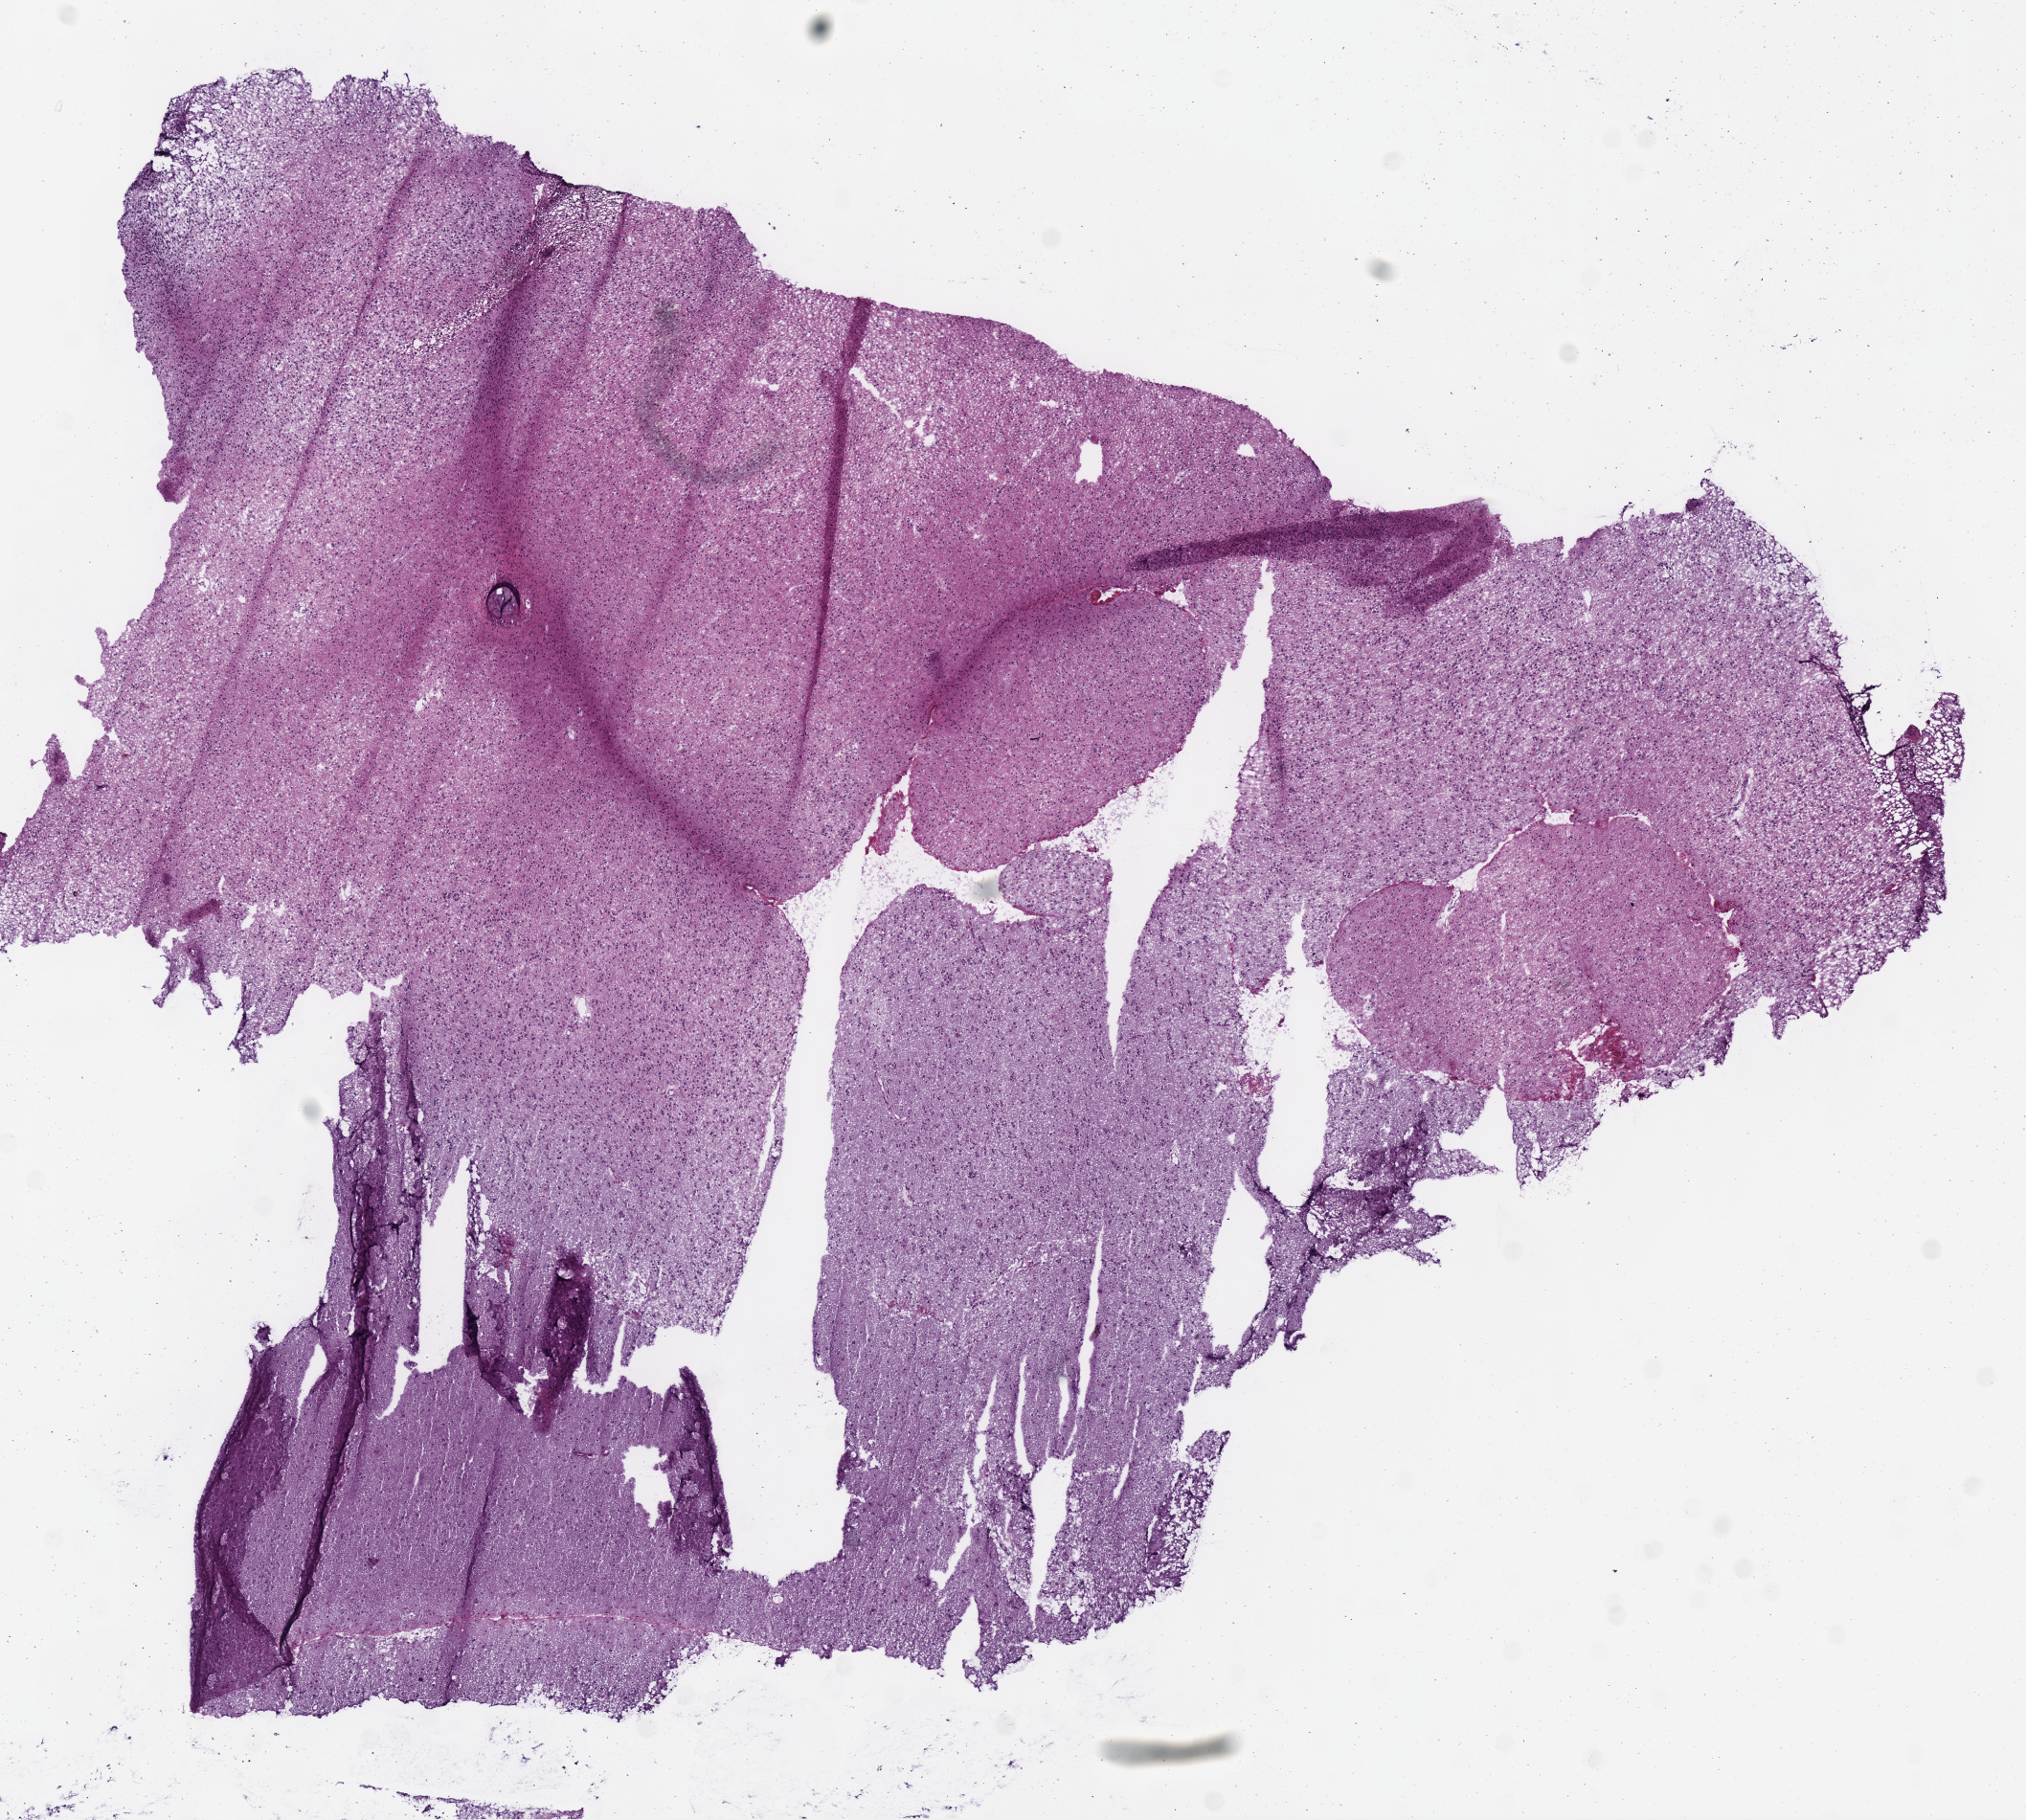
H&E-stained whole-slide image — a low-resolution overview of the entire scanned area, about 8.3 x 7.5 mm (from a 40x scan); frozen section from the top of the tissue portion; sample: primary tumour, brain. Male, age 64 years at initial diagnosis. Histologic grade: G3 (poorly differentiated). Pathologist review of this section (percent, as recorded): tumour cells 100%, tumour nuclei 75%, normal cells 0%, stromal cells 0%, necrosis 0%.
- pathologic diagnosis: Oligodendroglioma, anaplastic (cerebrum)
- laterality: right